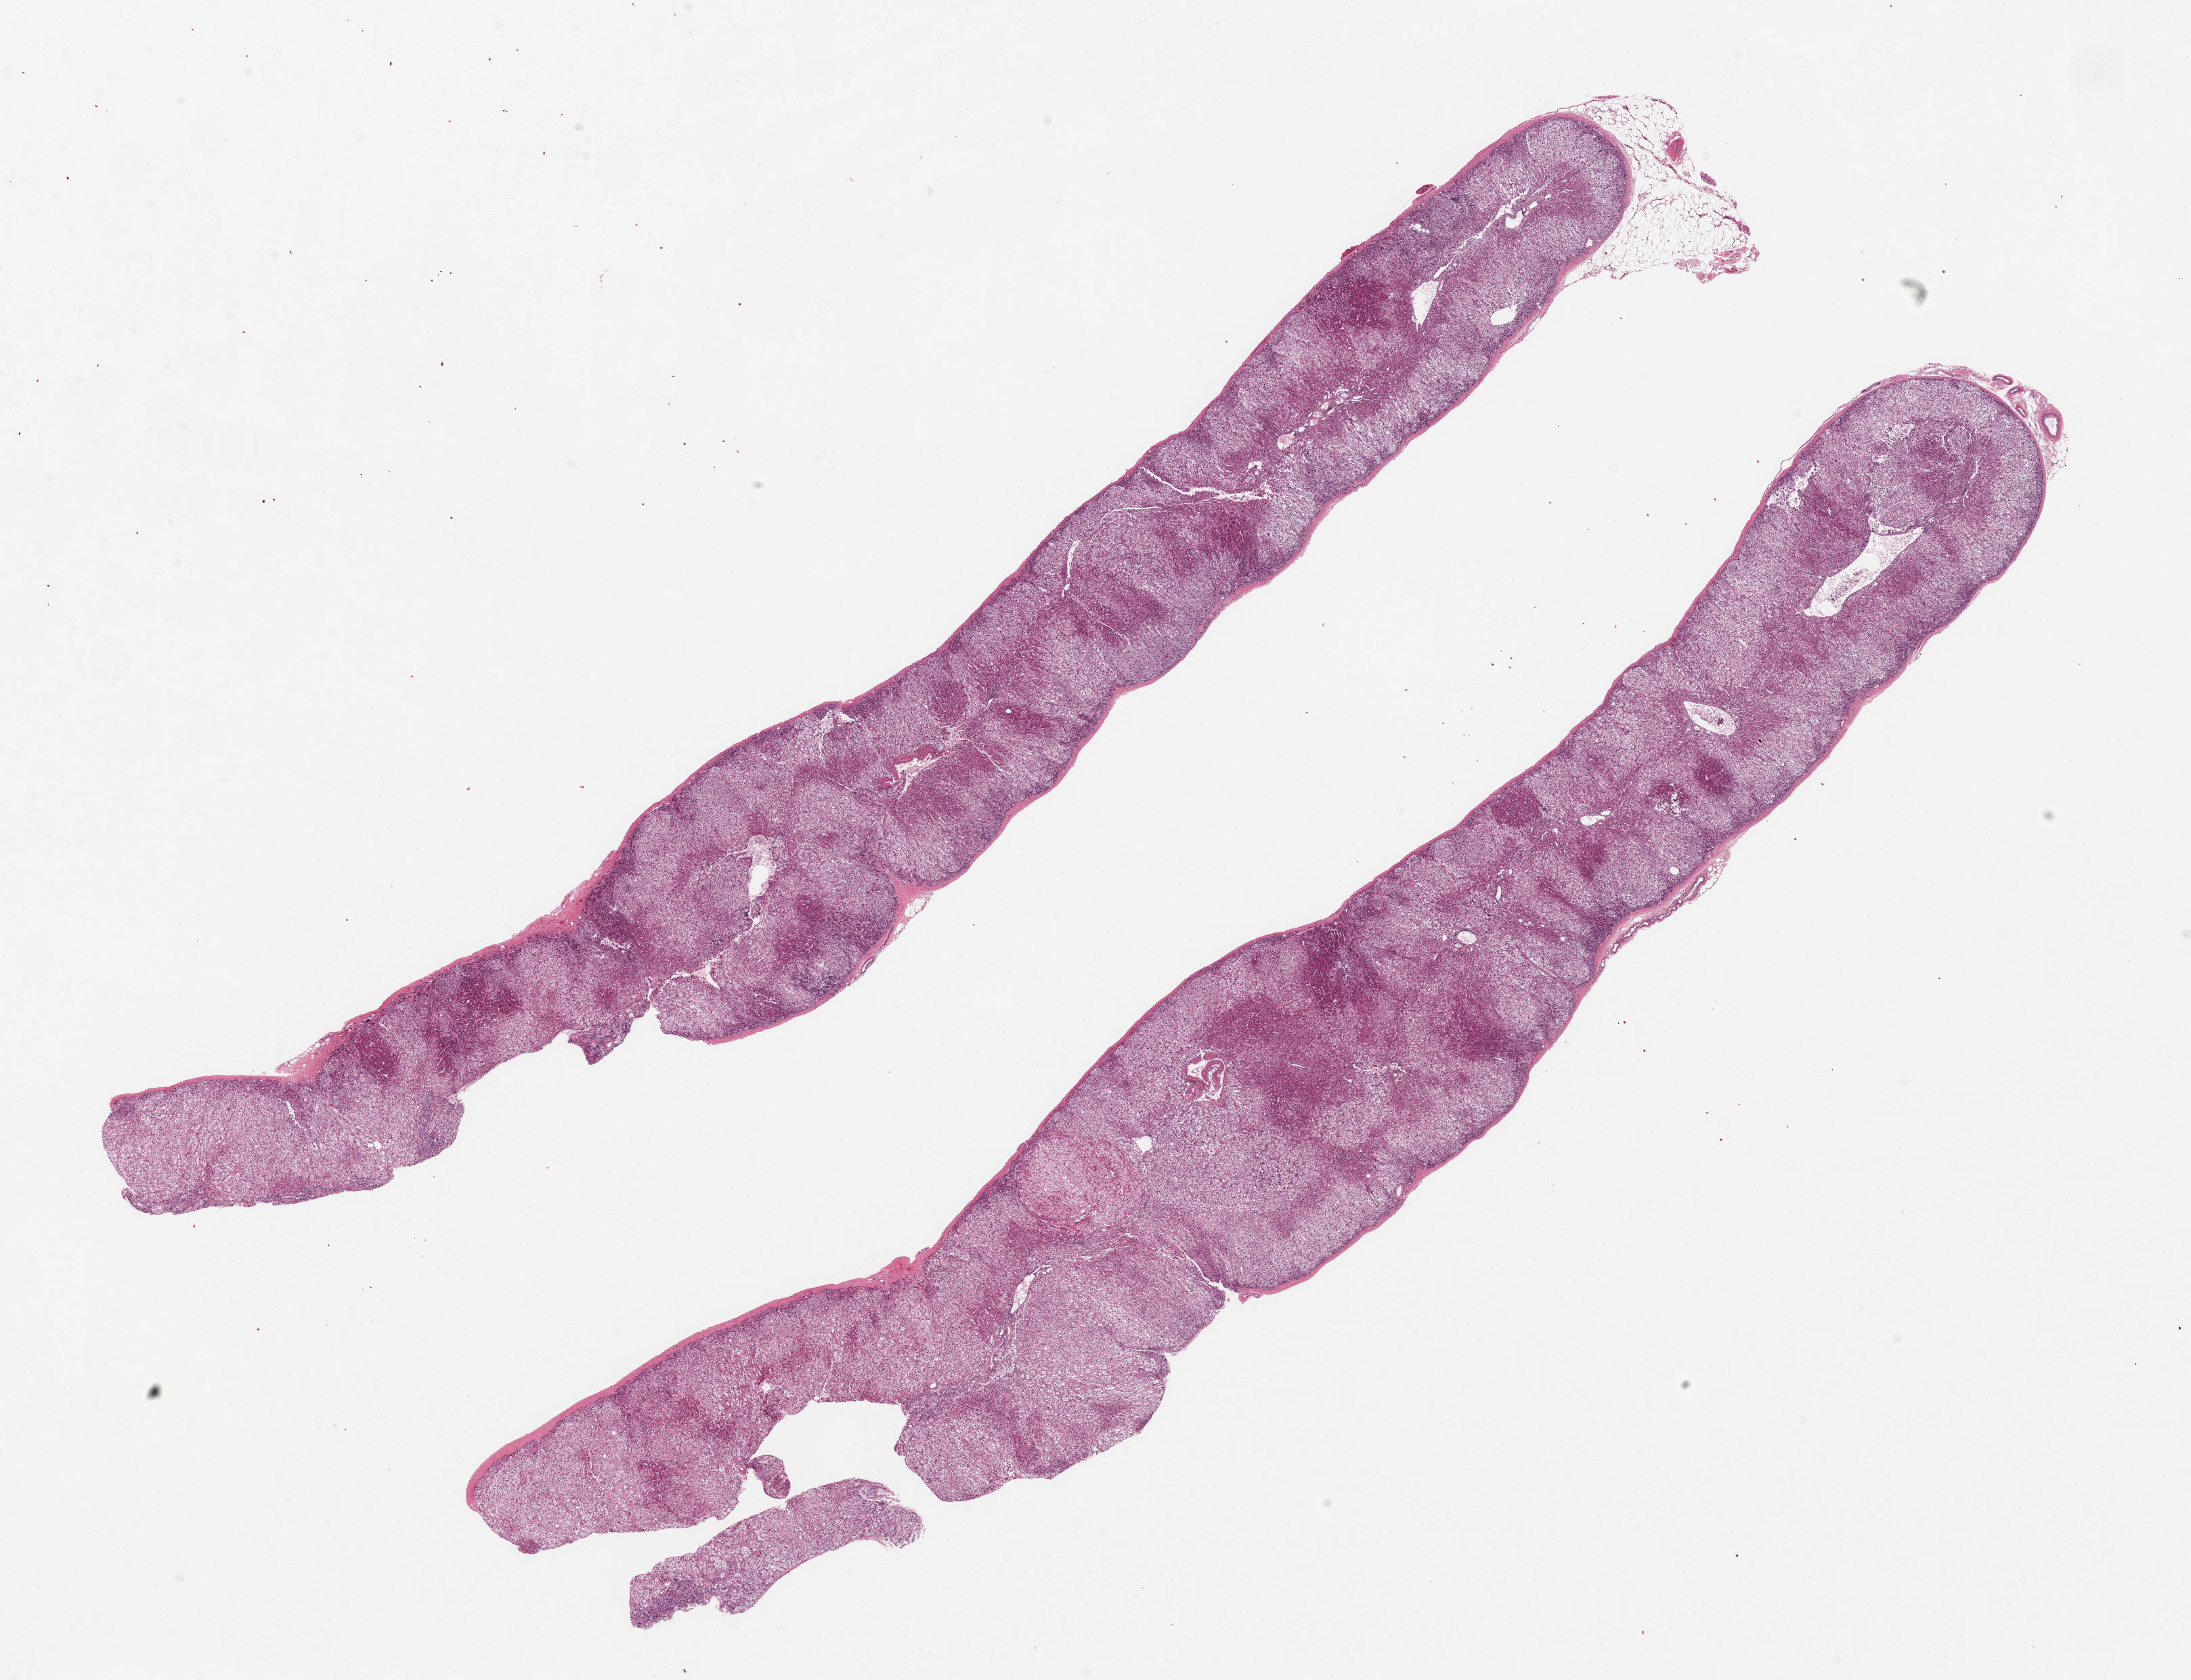
Whole-slide image, hematoxylin and eosin (H&E) stain — whole scanned area (about 25.6 x 19.6 mm, acquisition: 20x scan) shown as a low-resolution overview. PAXgene-fixed paraffin-embedded (PFPE) section. Target tissue: adrenal gland. Tissue donor sample. Donor sex: male.
Reviewer comment on this tissue sample: 2 ~22x3mm aliquots, clean, well-preserved.